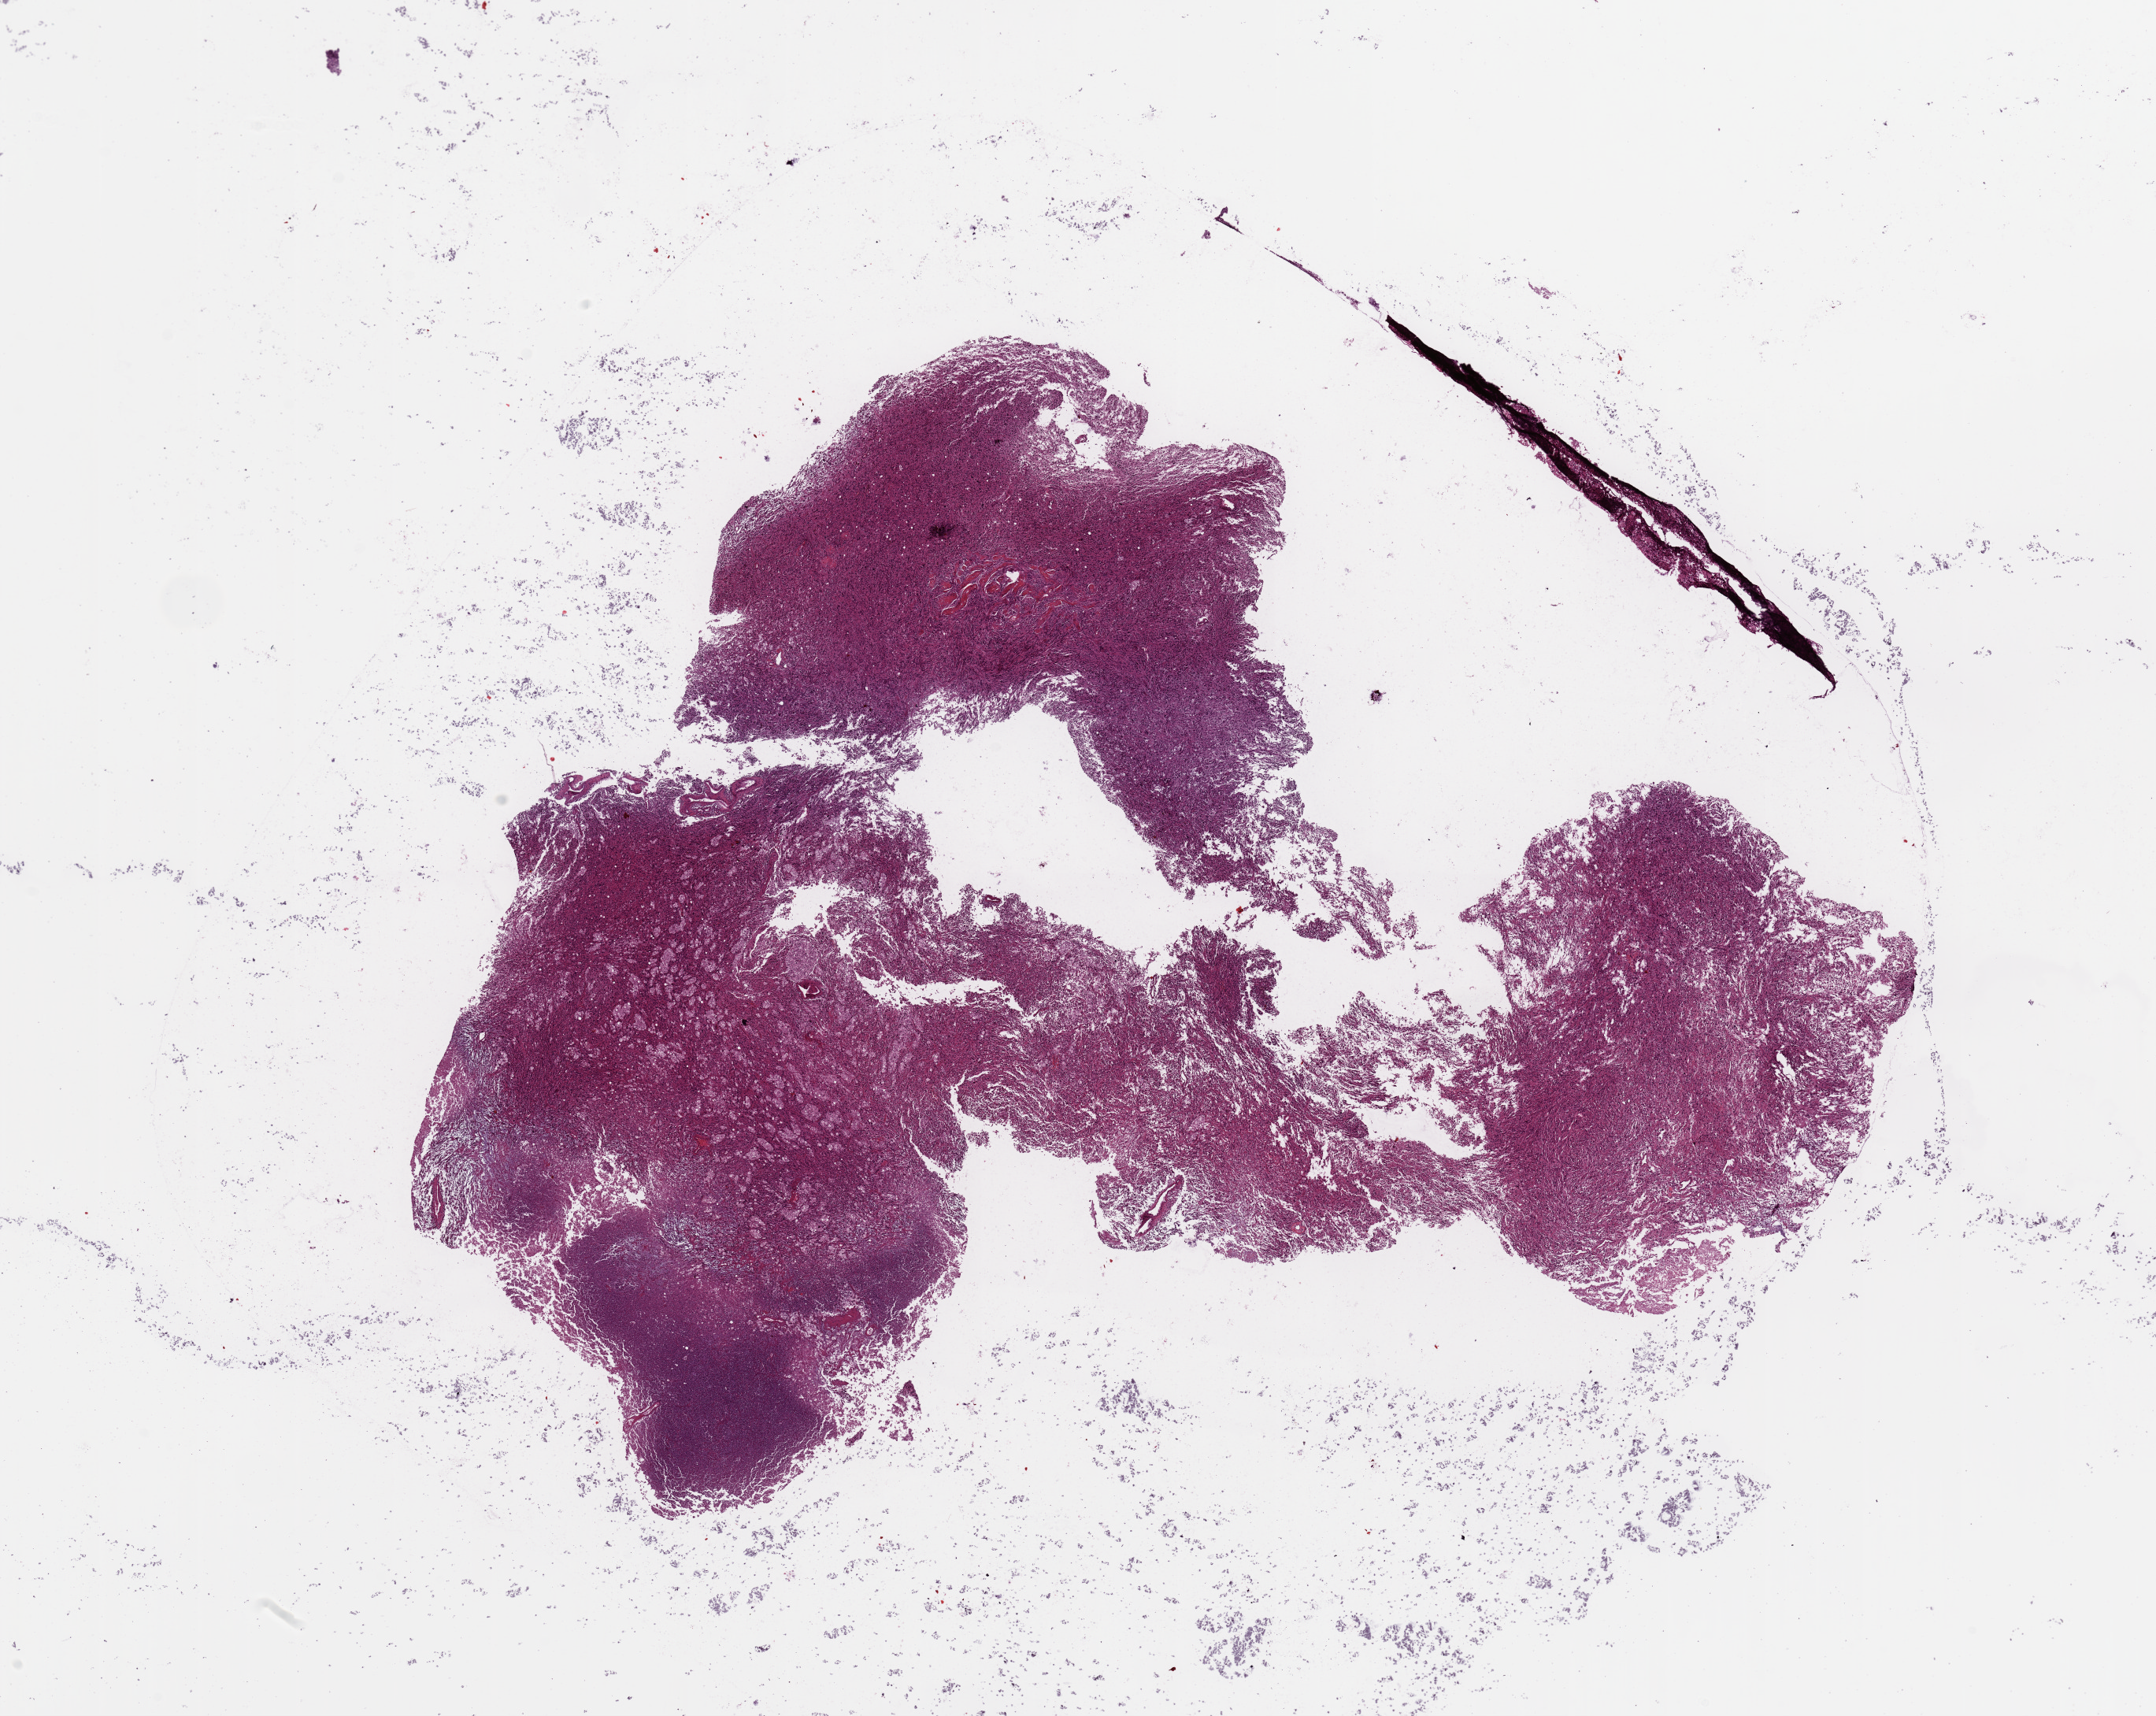
Digitized Hematoxylin and eosin (H&E) stained tissue section (whole slide), whole scanned area (about 21.7 x 17.2 mm, slide scanned at 20x) shown as a low-resolution overview; tumour tissue sample, sampled site: brain. Female, 24 y/o.
Diagnosis: Glioblastoma.